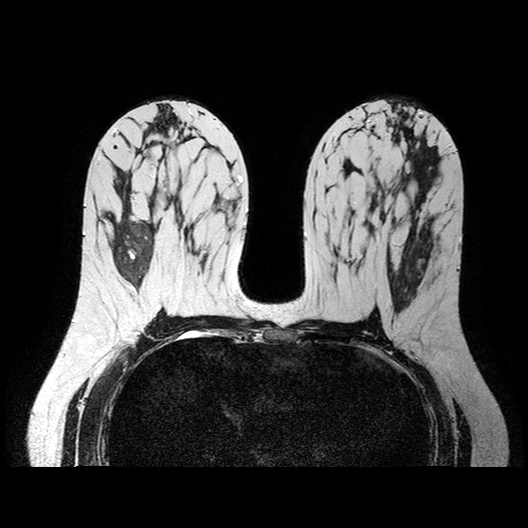
Breast MRI examination; 2 images, each one mid-volume slice chosen by position.
Image 1: axial T2-weighted / STIR image, series "T2W_TSE SENSE", slice 44 of 86.
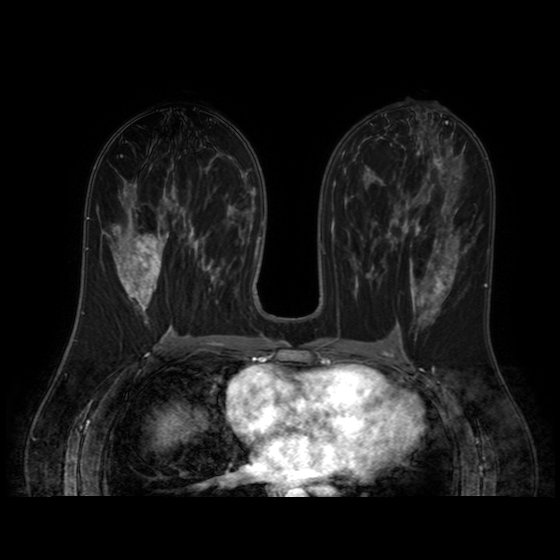
Image 2: axial dynamic contrast-enhanced T1-weighted image, series "AX BLISS_AUTO SENSE", slice 44 of 86, dynamic phase 5 of 8.
Pathology recorded for this patient (not read from these images): pathology diagnosis: stromal hyperplasia no CA (right breast).